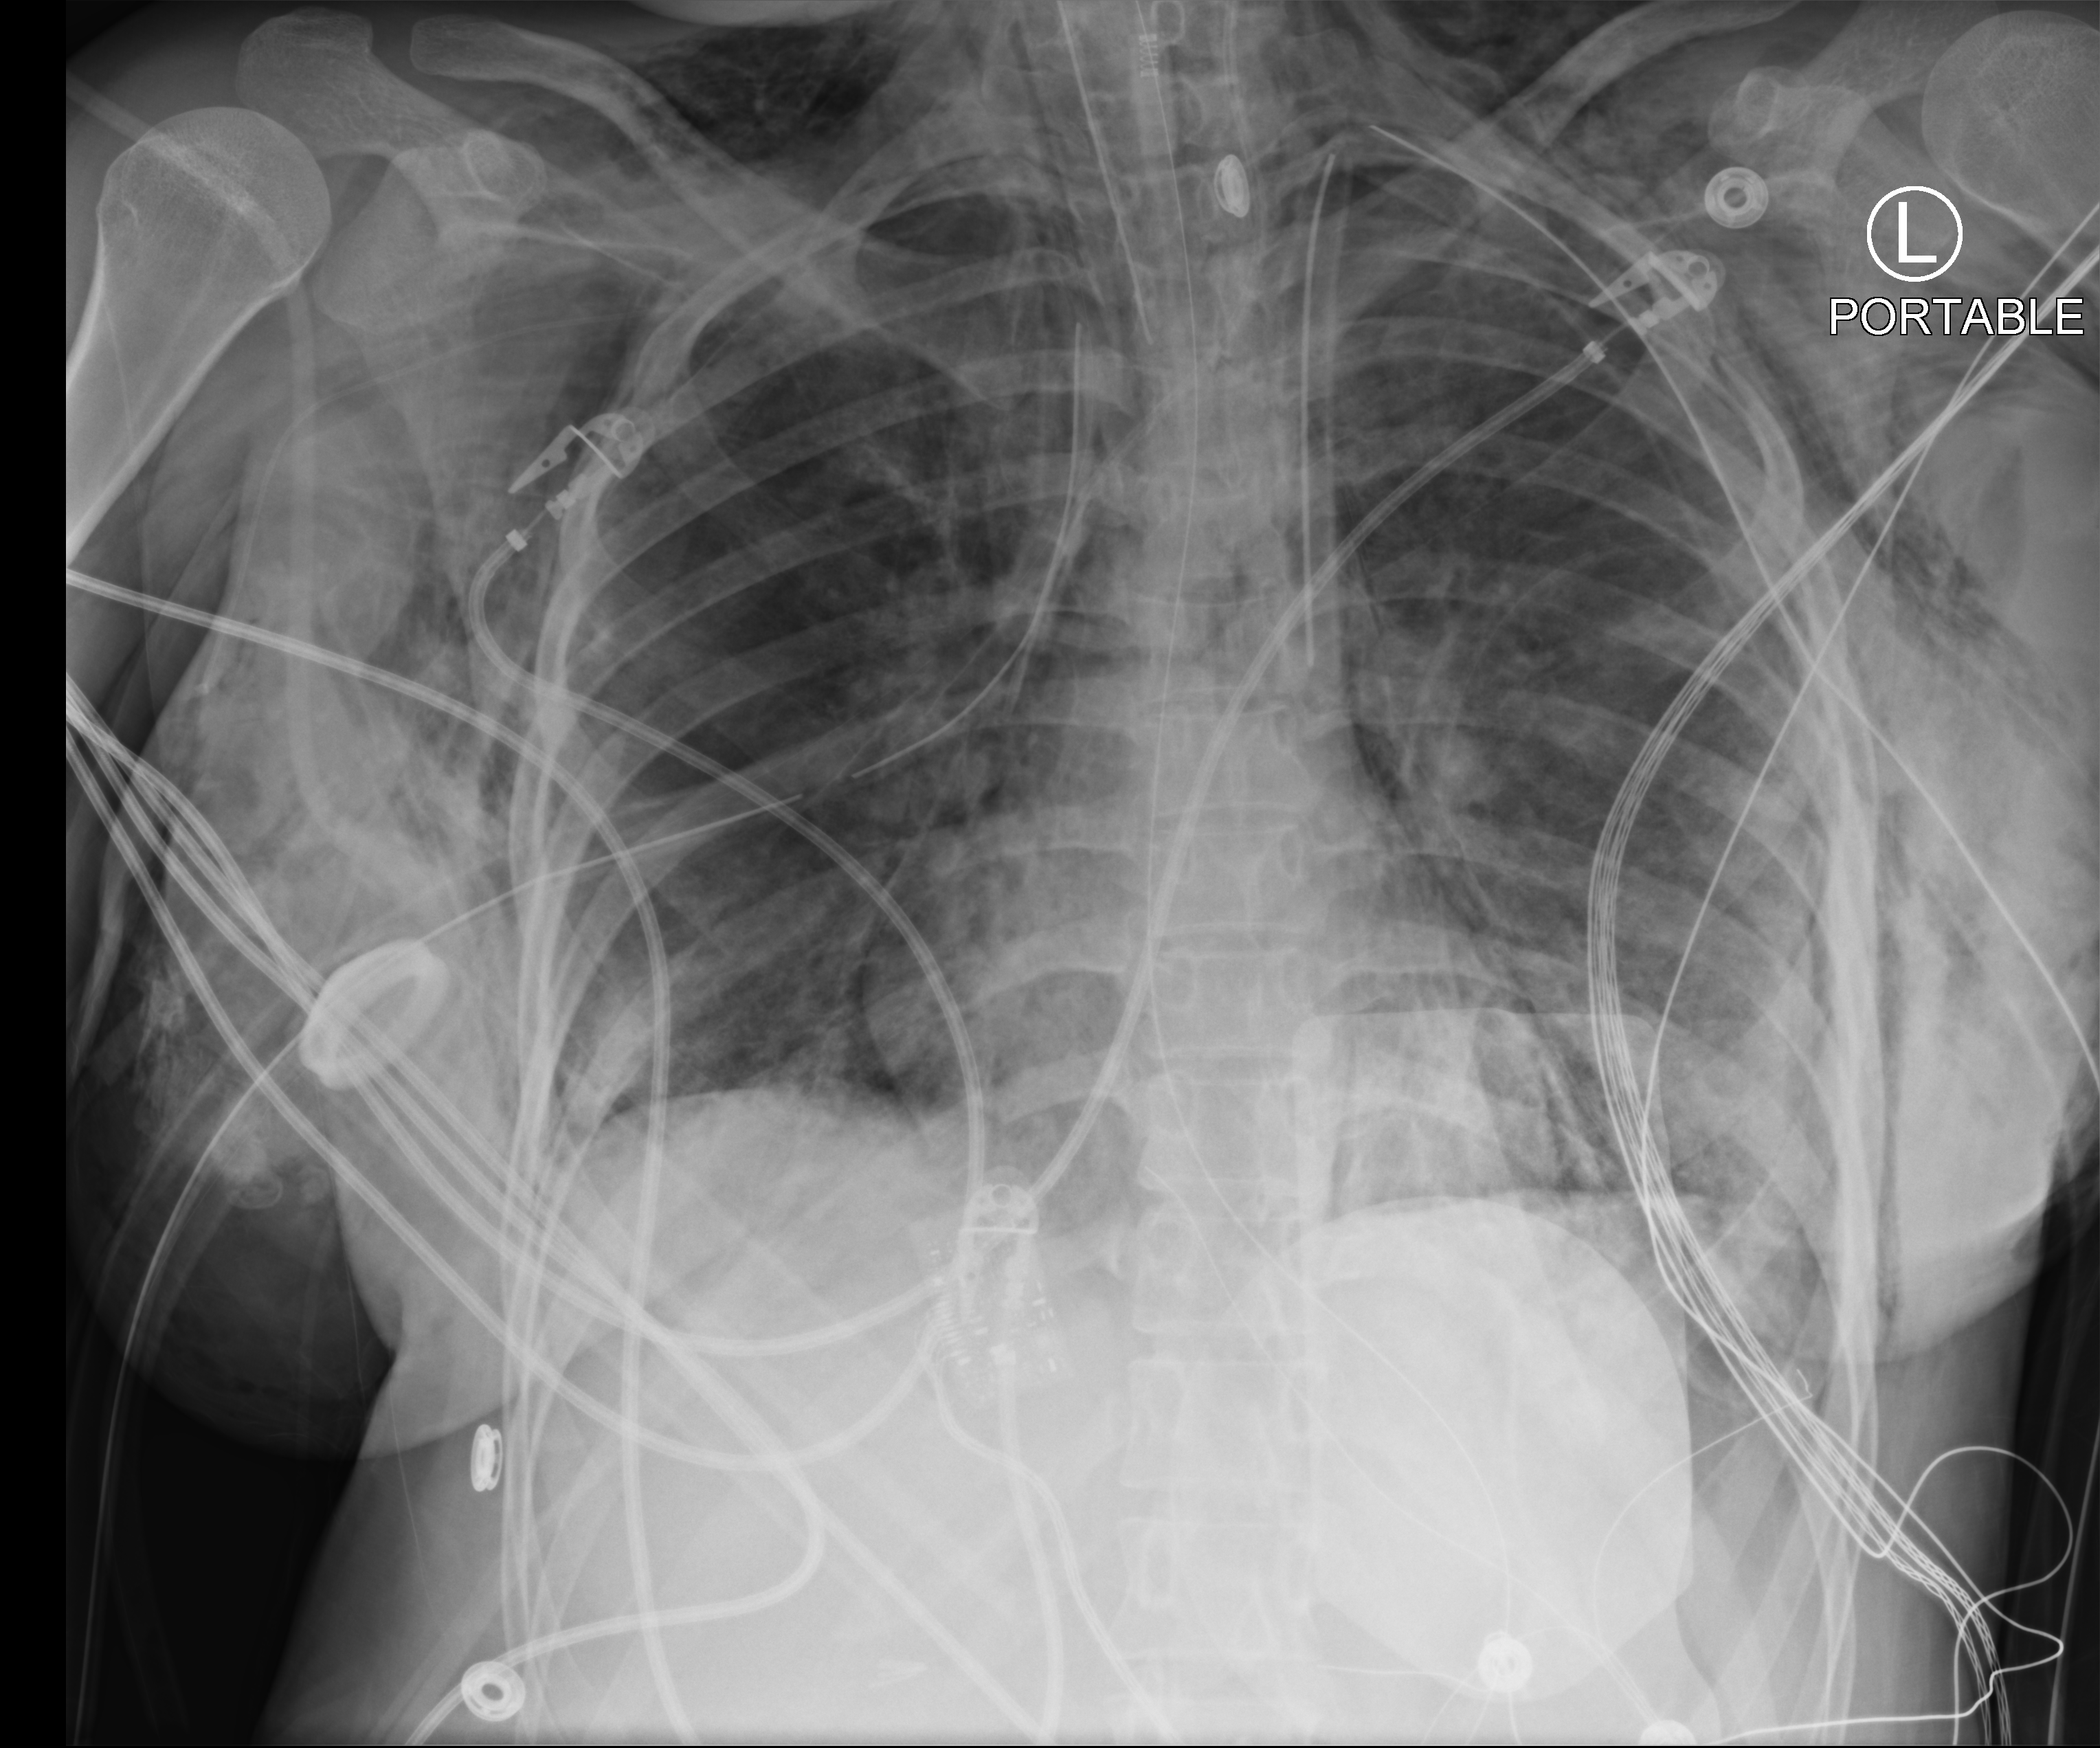
Chest X-ray (portable). Patient hospitalised with COVID-19, aged 18–59 years.
From the hospital-stay record, not from the radiograph (when in the stay this image was taken is not recorded): smoking status (admission record): never; chronic kidney disease (admission record): no; mechanically ventilated during this hospital stay: yes.